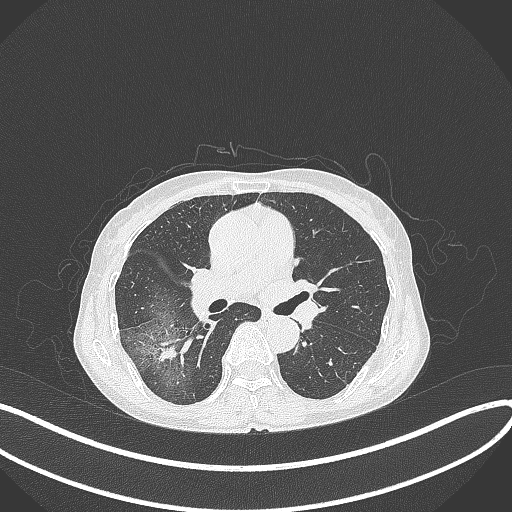
Chest CT, one axial slice; slice 223 of 371 in the series (ordered by position); reconstruction kernel B70f; 120 kVp; lung window (W 1500 / L -600 HU); 512 × 512 image matrix, field of view 400 × 400 mm. Female patient, age 69 years. From the clinical record (not read from this slice): clinical TNM (as recorded): T1b N0 M0.
Outlined on this slice (bounding box drawn by a radiologist):
- lung tumour (recorded histology: adenocarcinoma): bounding box [x1, y1, x2, y2] px = [153, 335, 180, 366]